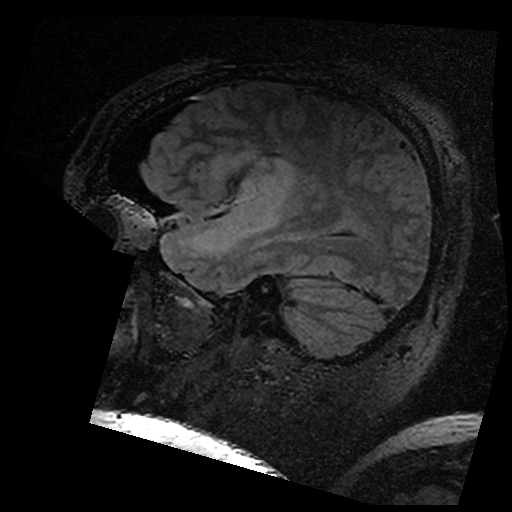
Brain MRI from a brain-tumour surgery series, one sagittal slice. Position 125 of 176 along the scan axis. T2 FLAIR. 1 mm slice thickness. 512 × 512 image matrix, field of view 250 × 250 mm. Case-level facts recorded for this patient, not image findings: histopathology: Astrocytoma; WHO grade: 3; IDH mutation: yes; tumour location: Left Insular.
Structures marked on this image (expert manual segmentation):
- residual tumour: bounding box <215,150,293,199> (left, top, right, bottom; pixels)